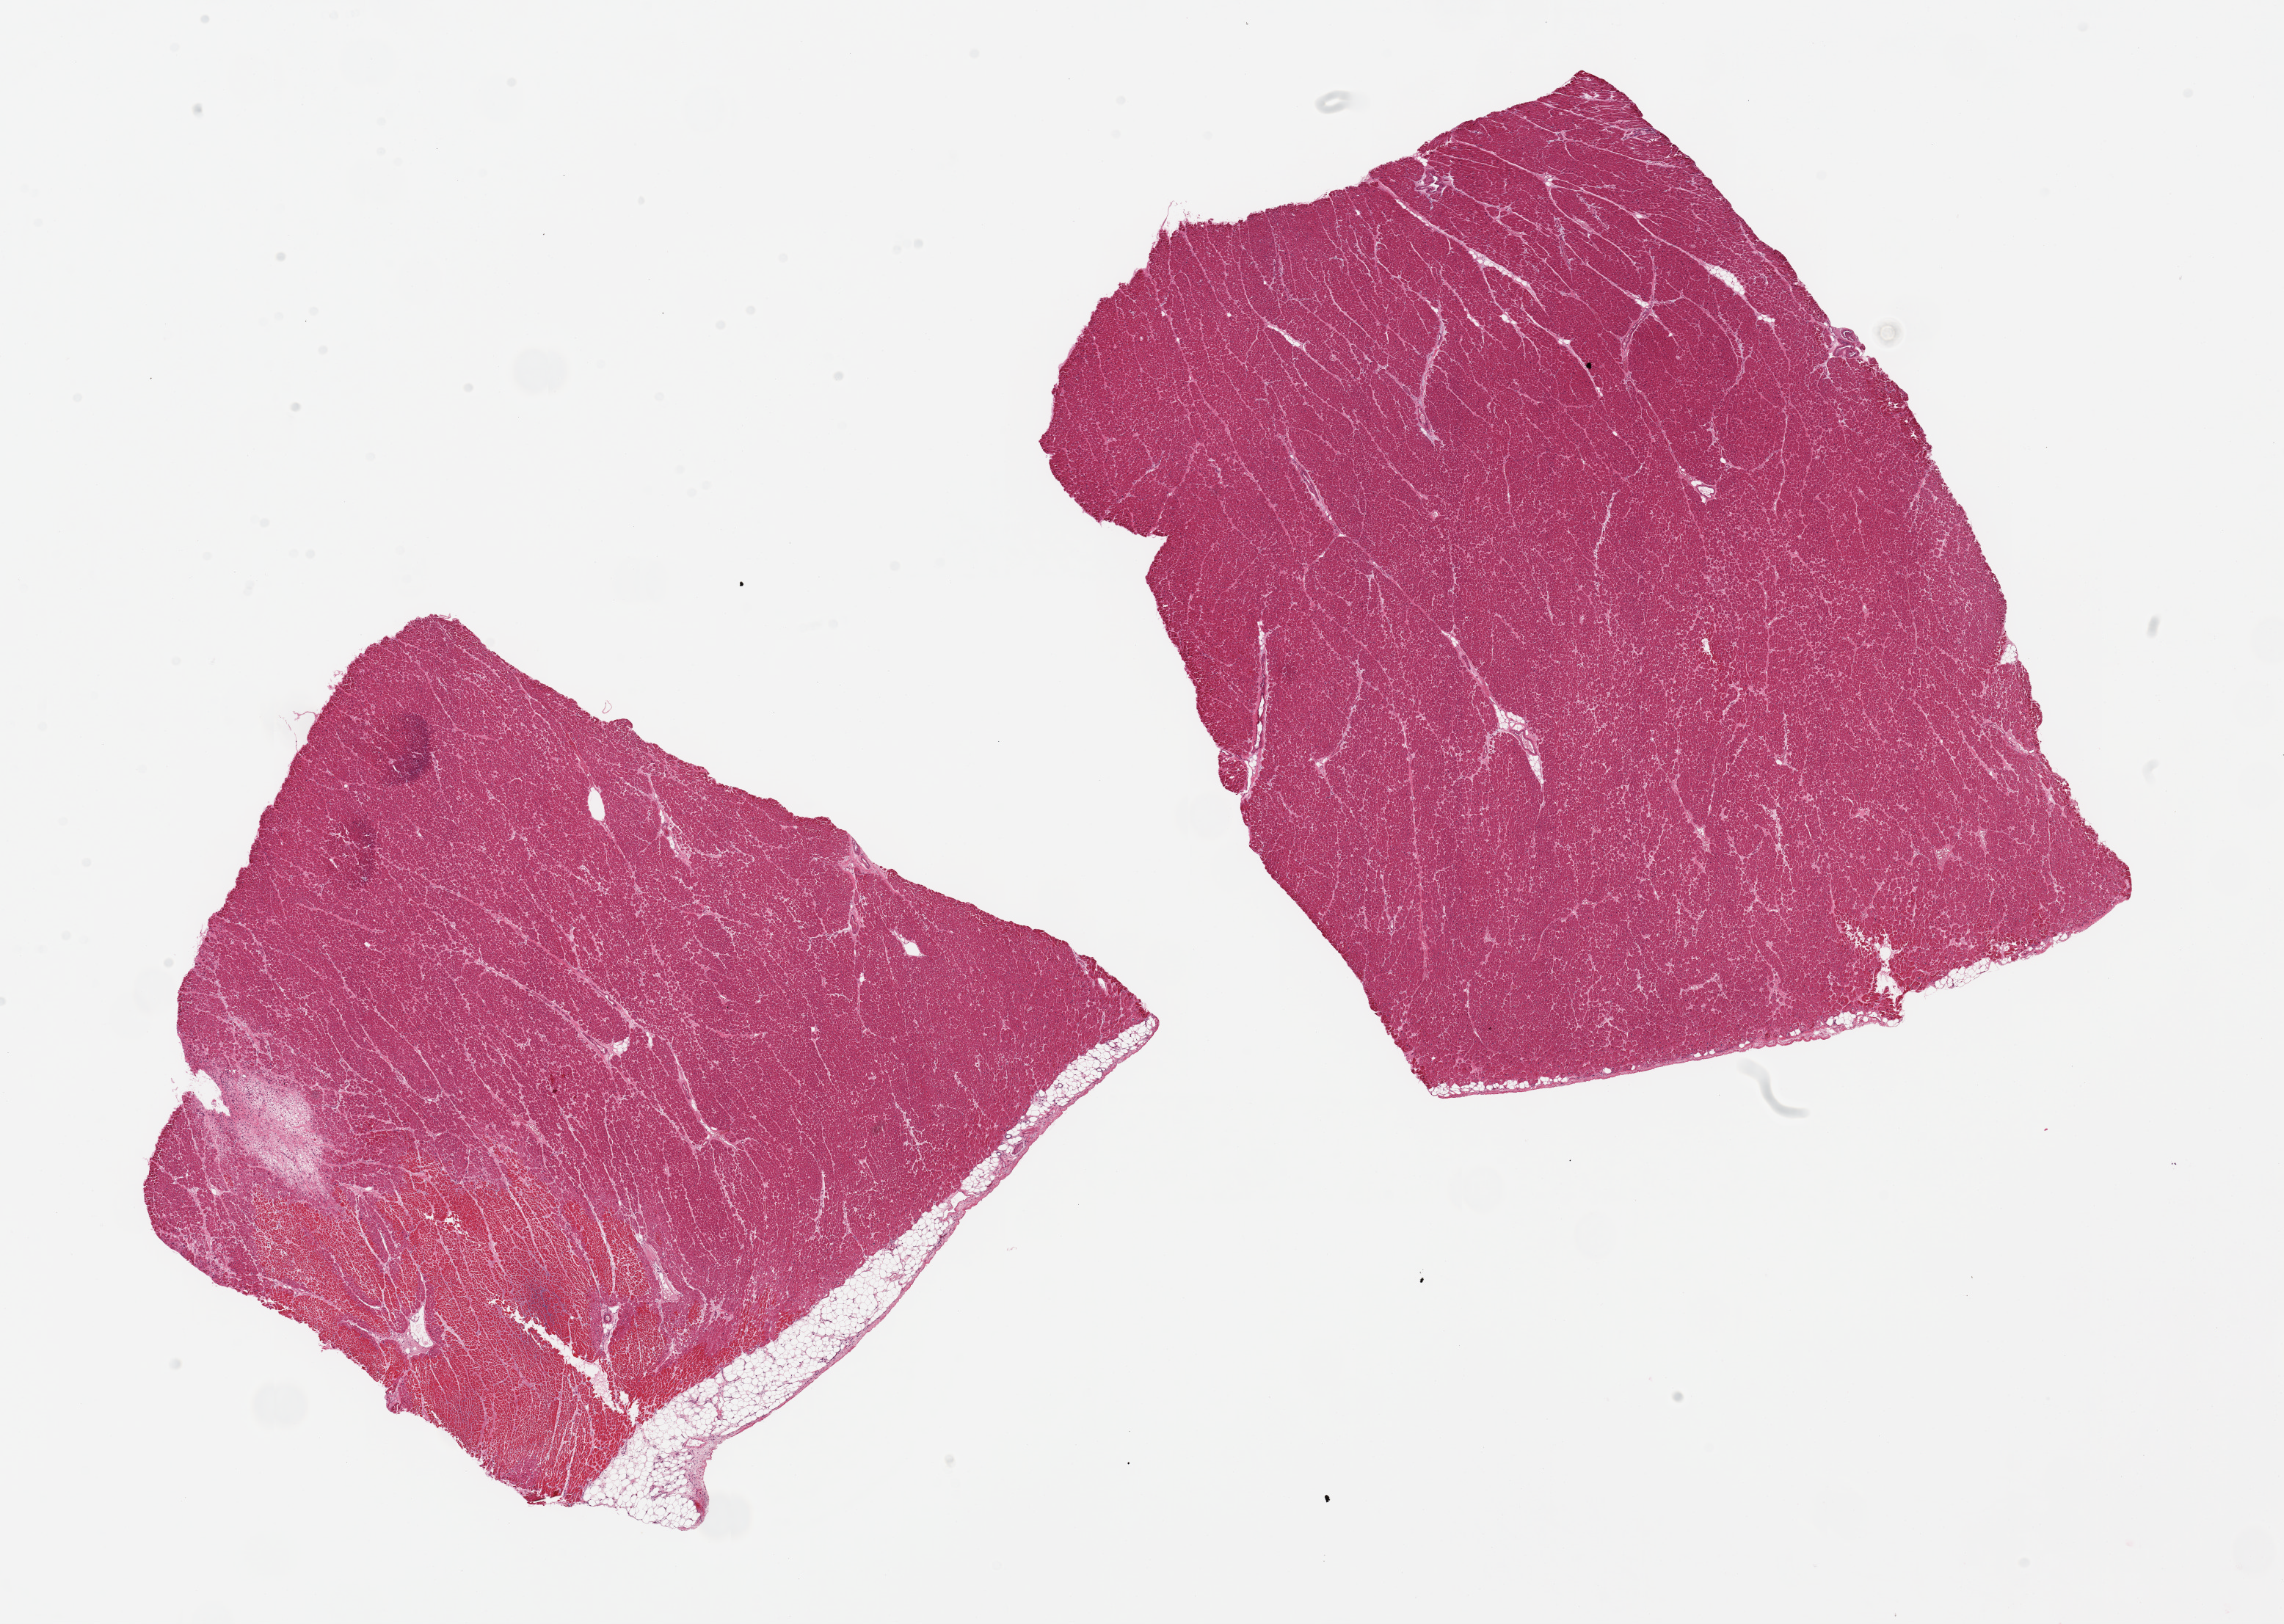
Hematoxylin and eosin (H&E) whole-slide image — shown as a low-resolution overview of the whole scanned area (about 24.6 x 17.5 mm). PAXgene-fixed paraffin-embedded (PFPE) section. Target tissue: heart. Tissue donor sample. Donor sex: female.
Pathologist's review note for this sample: 2 pieces, 9.5x8 & 11x8mm; 2 mm subacute infarct, in one aliquot.